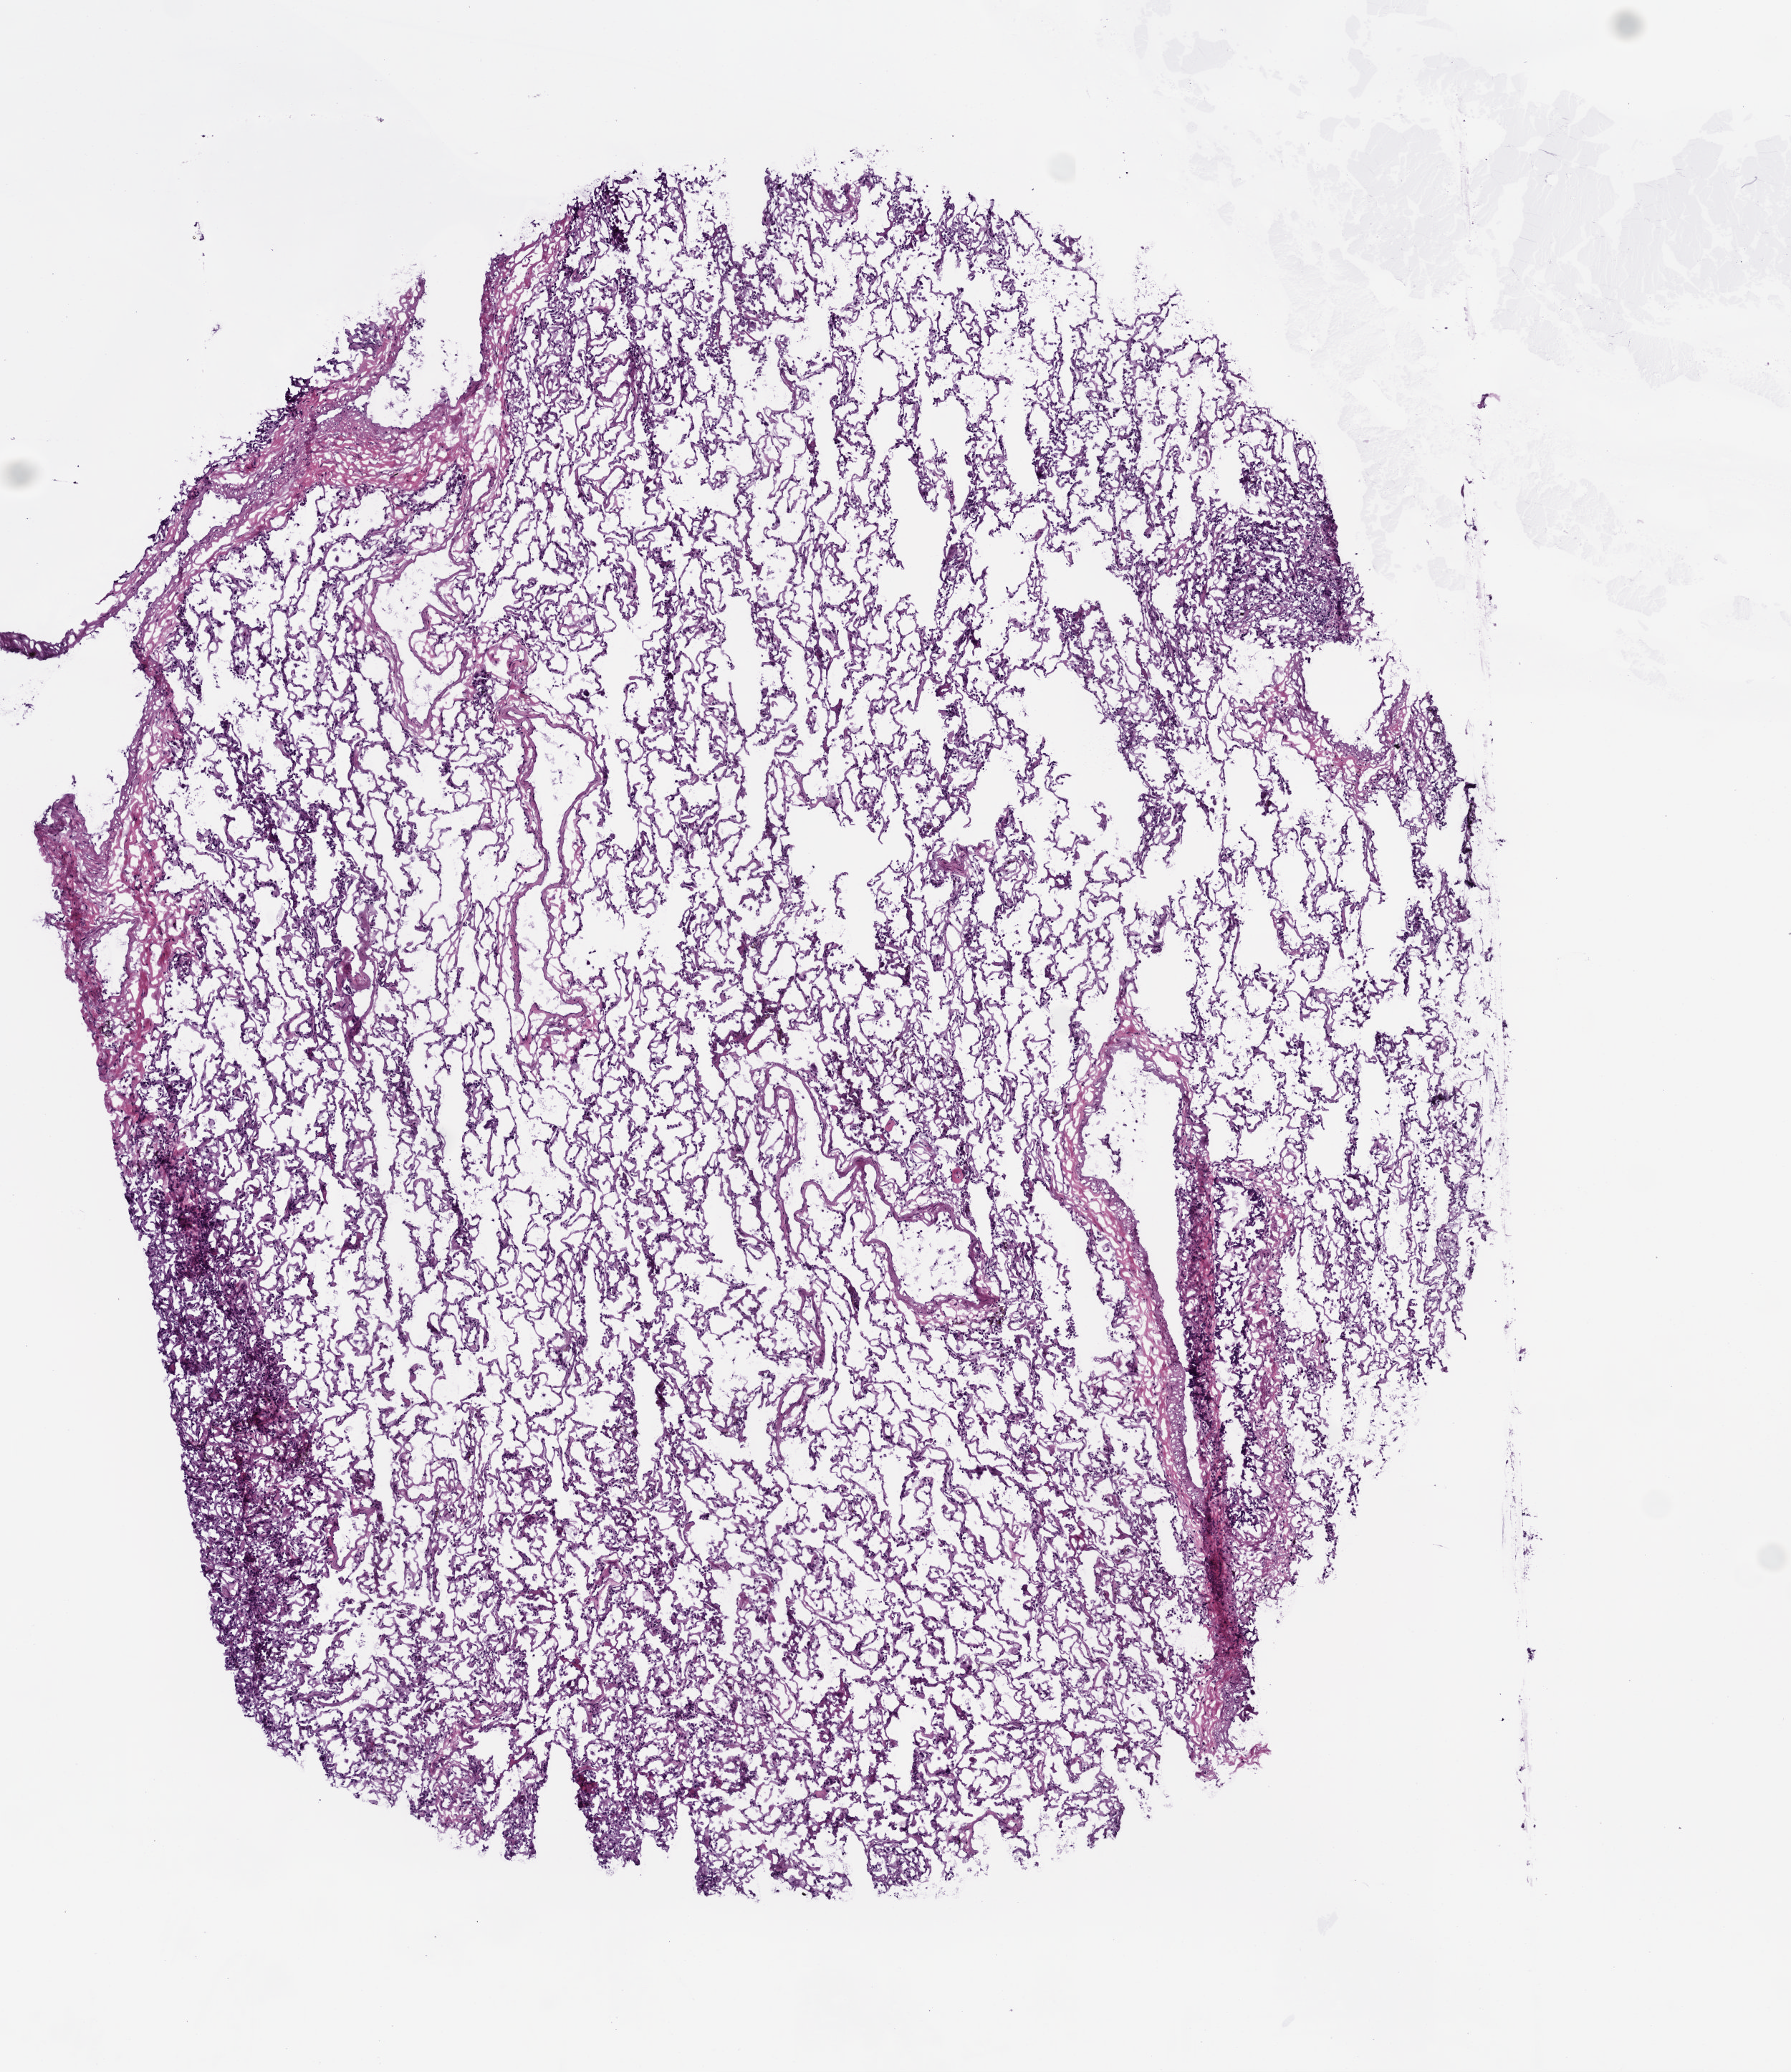
Whole-slide histology image, H&E-stained — whole scanned area (about 5.0 x 5.8 mm) shown as a low-resolution overview; frozen section from the top of the tissue portion; lung, solid tissue normal (non-tumour tissue) sample. Male patient; age at initial diagnosis 50 years.
* this section: solid tissue normal sample (biorepository sample class)
* patient diagnosis: Squamous cell carcinoma, NOS (lower lobe, lung)